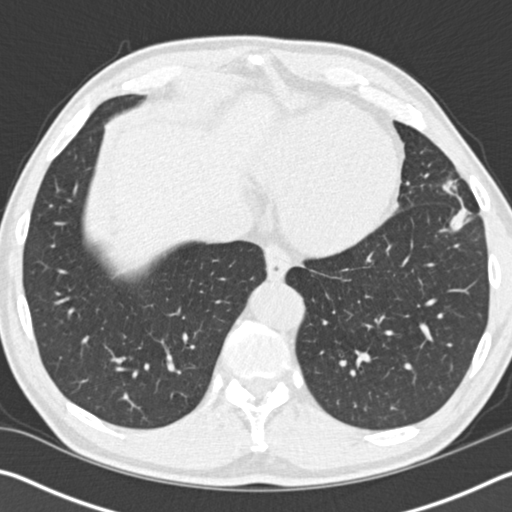
Low-dose screening chest CT, one axial slice; position 39 of 162 along the scan axis; lung window (W 1500 / L -600 HU); 2 mm slice thickness; 512 × 512 image matrix.
Annotated regions visible in this slice (outlined manually by an expert reader):
- lesion 1 (tumor, upper lobe of left lung): box from (x=442, y=180) to (x=470, y=232) px